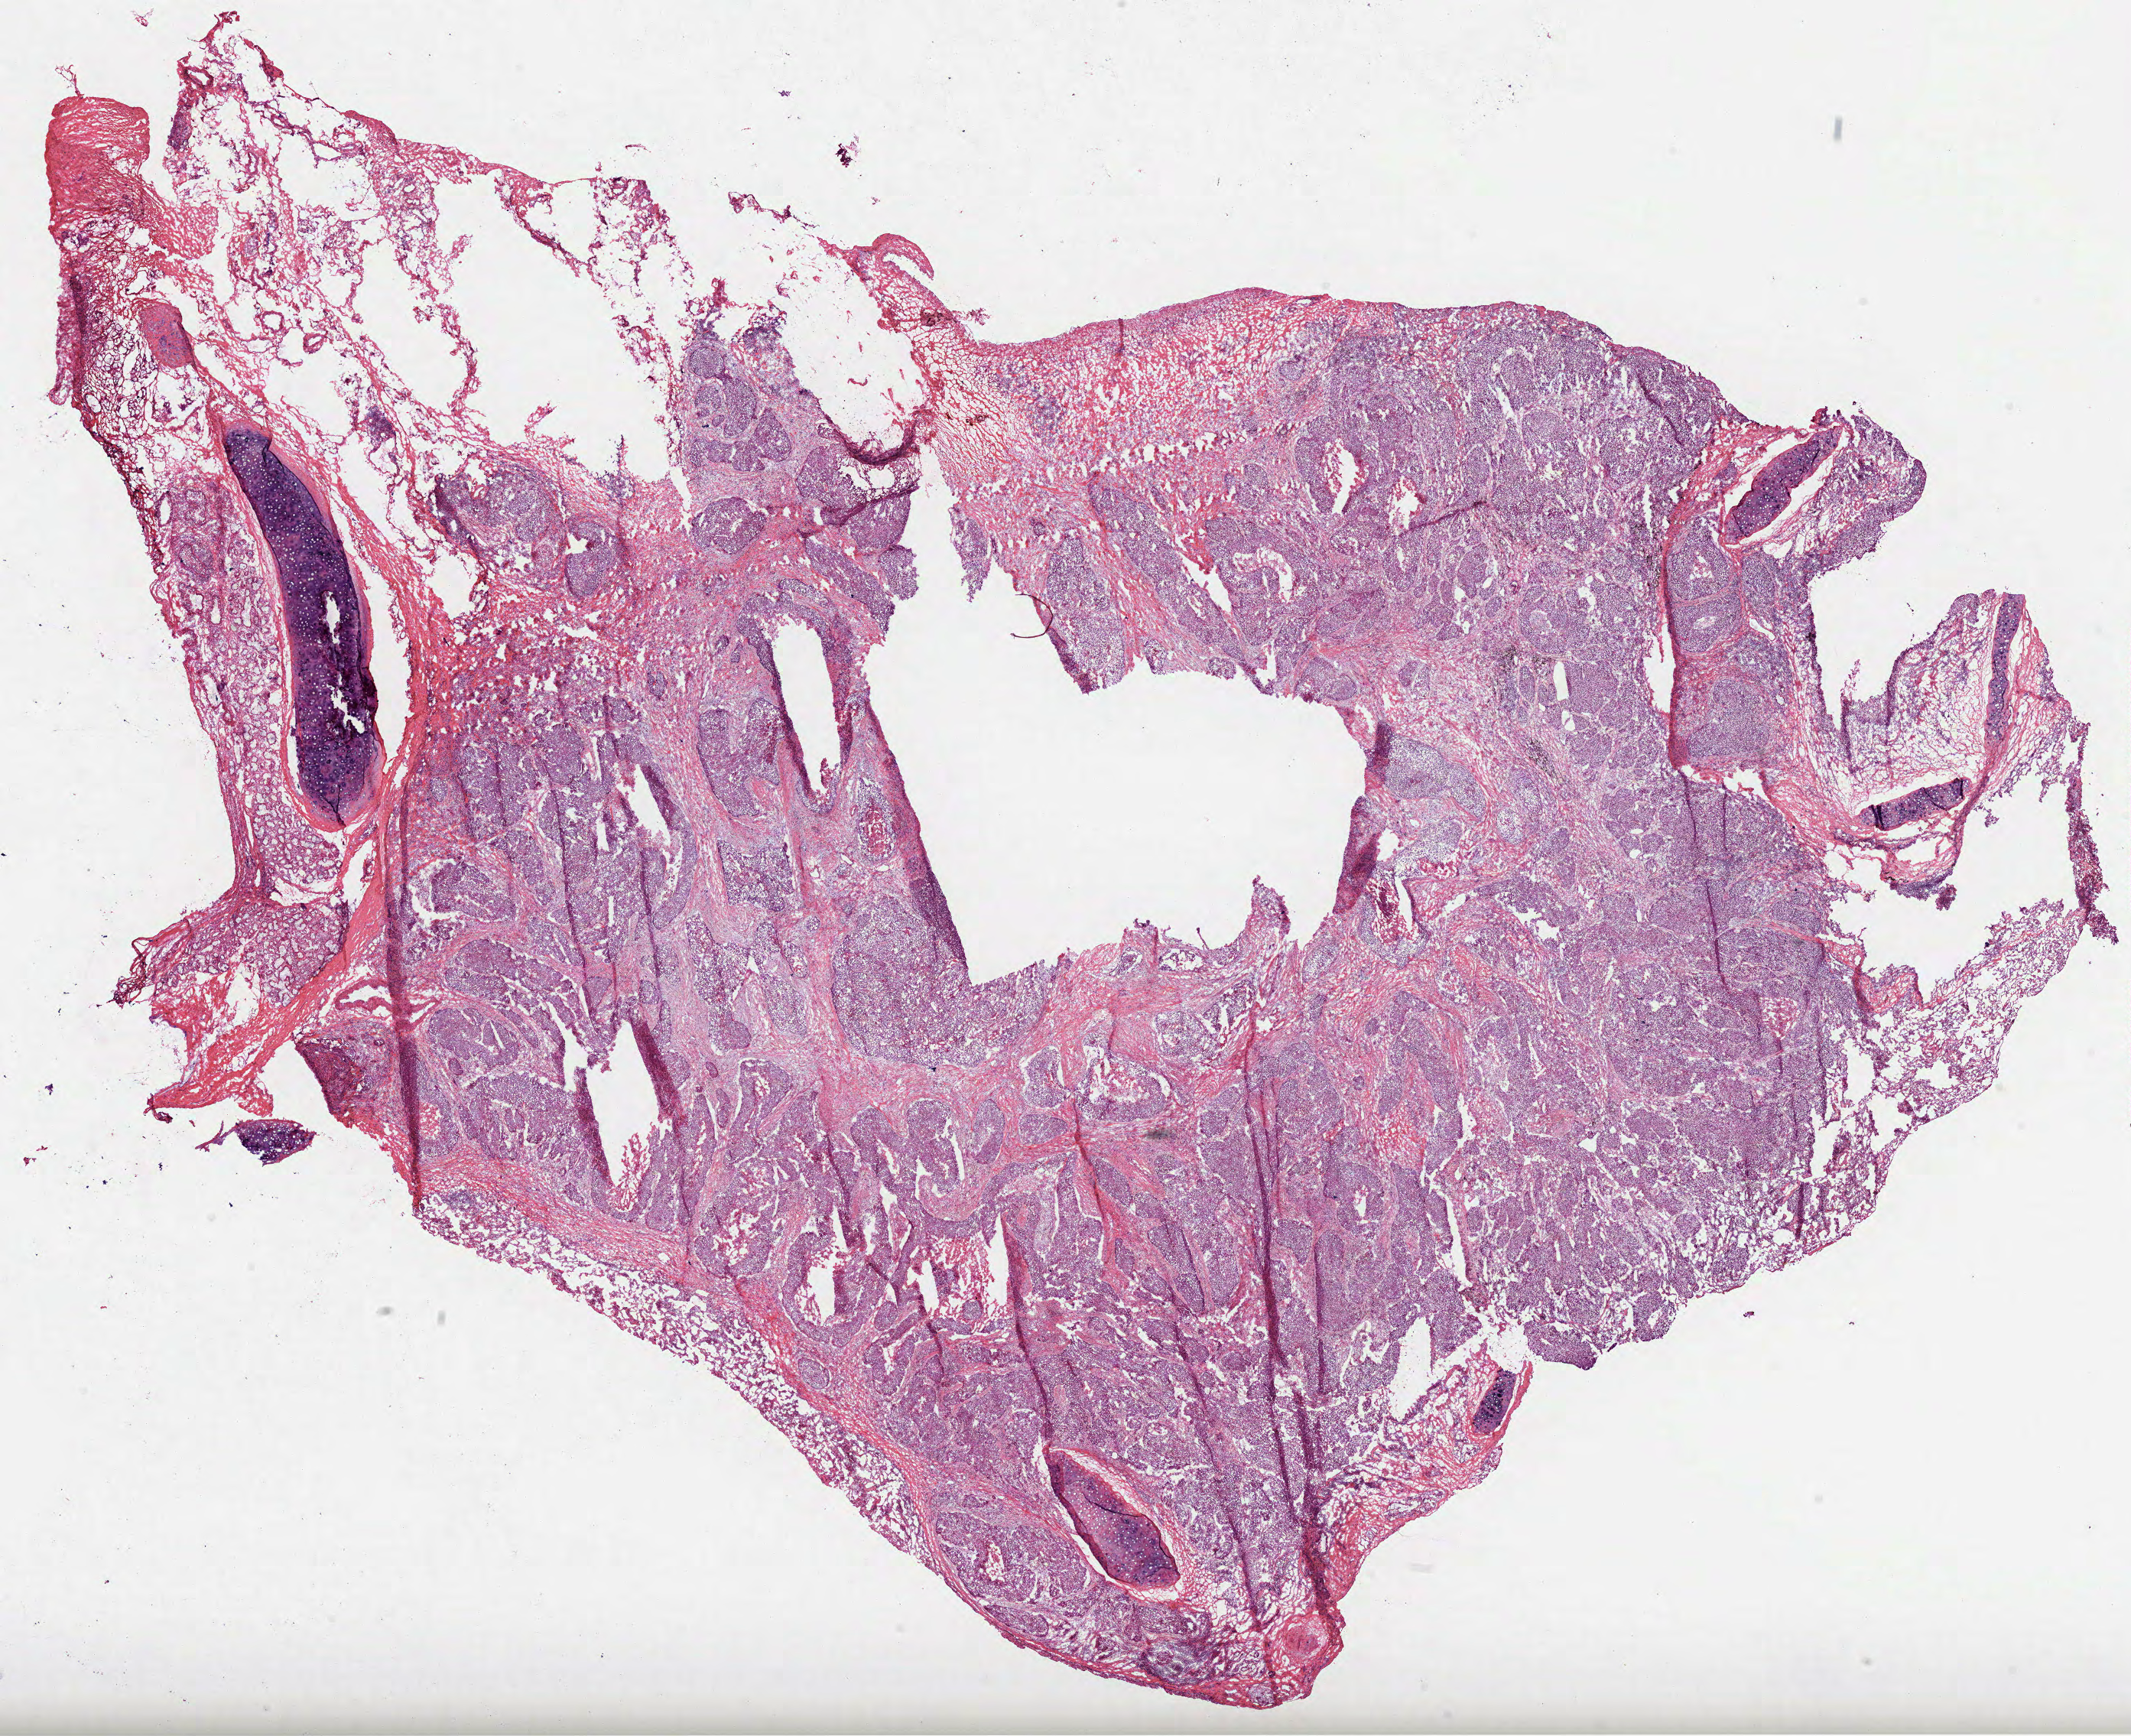
Hematoxylin and eosin (H&E) stained whole-slide image, low-resolution overview of the scanned area, about 22.5 x 18.3 mm, frozen section, lung, primary tumour sample. Male patient; age at initial diagnosis 64 years. Pathologist review of this section (percent, as recorded): tumour cells 65%, tumour nuclei 70%.
Pathologic diagnosis: Squamous cell carcinoma, NOS (upper lobe, lung).